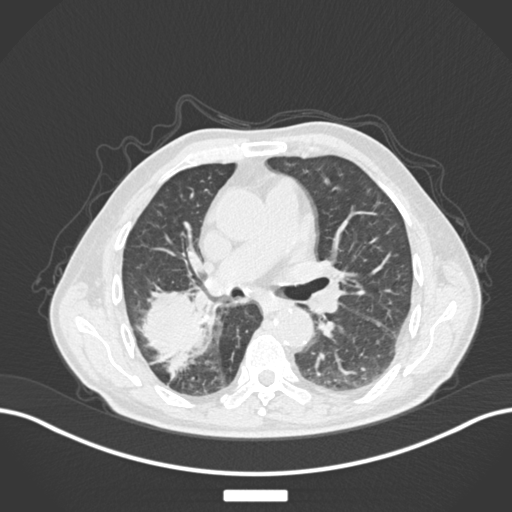
Chest CT, one axial slice. Slice 96 of 201 in the series (ordered by position). Reconstruction kernel B30f. 120 kVp. Lung window (W 1500 / L -600 HU). 1 mm slice thickness. 512 × 512 image matrix. Patient: male, 72 years. From the clinical record (not read from this slice): clinical TNM (as recorded): T3 N2 M0.
Structures marked on this image (bounding box drawn by a radiologist):
- lung tumour (recorded histology: adenocarcinoma): bounding box [x1, y1, x2, y2] px = [137, 282, 208, 378]